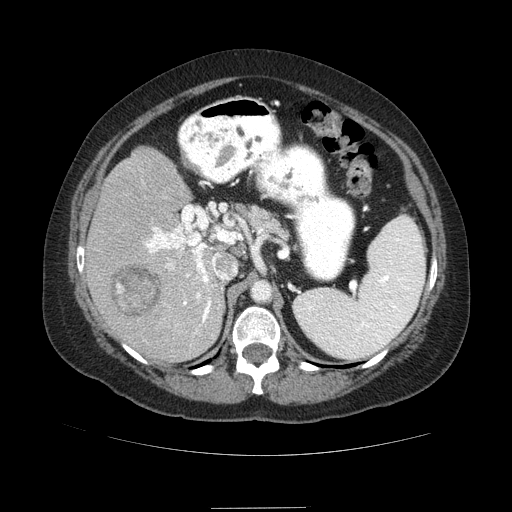
Contrast-enhanced abdominal CT (liver protocol), one axial slice; position 51 of 89 along the scan axis; reconstruction kernel STANDARD; 120 kVp; soft-tissue window (W 400 / L 40 HU); 2.5 mm slice thickness; 512 × 512 image matrix, field of view 400 × 400 mm. Case-level facts recorded for this patient, not image findings: diagnosis: hepatocellular carcinoma (patient treated with transarterial chemoembolisation; whether this scan precedes or follows treatment is not stated here); TNM stage (as recorded): Stage-IIIB; Child-Pugh class: A; tumour nodularity: multinodular.
Outlined on this slice (semi-automatic segmentation, software-assisted and operator-edited):
- liver parenchyma outside the tumour (the mass and vessels are separate outlines, so this box may not span the whole liver): bounding box (x1, y1, x2, y2) in pixels: (86, 146, 226, 362)
- mass: (109, 263, 161, 315)
- liver vessels: (144, 225, 221, 333)